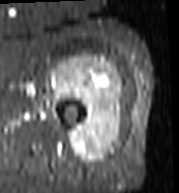
MRI of an extremity soft-tissue mass, one axial slice. STIR. MR volume resampled by the dataset authors to the PET/CT grid (not the native acquisition matrix). 3.27 mm slice thickness. 179 × 193 image matrix, field of view 175 × 188 mm. Female patient. Case-level facts recorded for this patient, not image findings: histological type: undifferentiated – high grade; grade: high; site of the primary tumour: left thigh.
Structures marked on this image (expert contour drawn on MRI and transferred to this co-registered scan by the dataset authors):
- gross tumour volume including surrounding oedema: bounding box <45,57,124,168> (left, top, right, bottom; pixels)
- gross tumour volume (mass): <47,64,122,164>